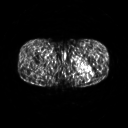
FDG PET of an extremity soft-tissue mass (from a PET/CT study), one axial slice; position 242 of 267 along the scan axis; 3.27 mm slice thickness; 128 × 128 image matrix, field of view 500 × 500 mm. Patient: male, 27 years. From the clinical record (not read from this slice): histological type: extraskeletal osteosarcoma; grade: high; site of the primary tumour: left adductur.
Annotated regions visible in this slice (expert contour drawn on MRI and transferred to this co-registered scan by the dataset authors):
- gross tumour volume (mass): bounding box (x1, y1, x2, y2) in pixels: (70, 61, 95, 75)